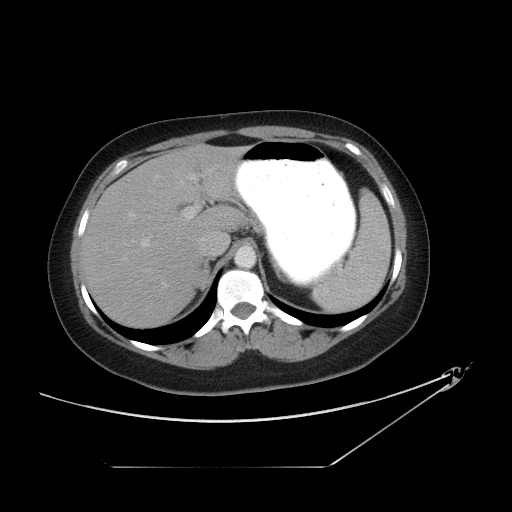
Contrast-enhanced abdominal CT, one axial slice; slice 74 of 90 in the series (ordered by position); intravenous contrast given; soft-tissue window (W 400 / L 40 HU); 5 mm slice thickness; 512 × 512 image matrix. Patient: female, 45 years. Case-level facts recorded for this patient, not image findings: diagnosis: adrenocortical carcinoma; tumour side: right adrenal; tumour size at pathology: 2.5 cm; Ki-67 index: 25 %; stage (as recorded): 1.
Outlined on this slice (semi-automatically segmented with operator editing):
- mass: bounding box [x1, y1, x2, y2] px = [194, 271, 209, 289]